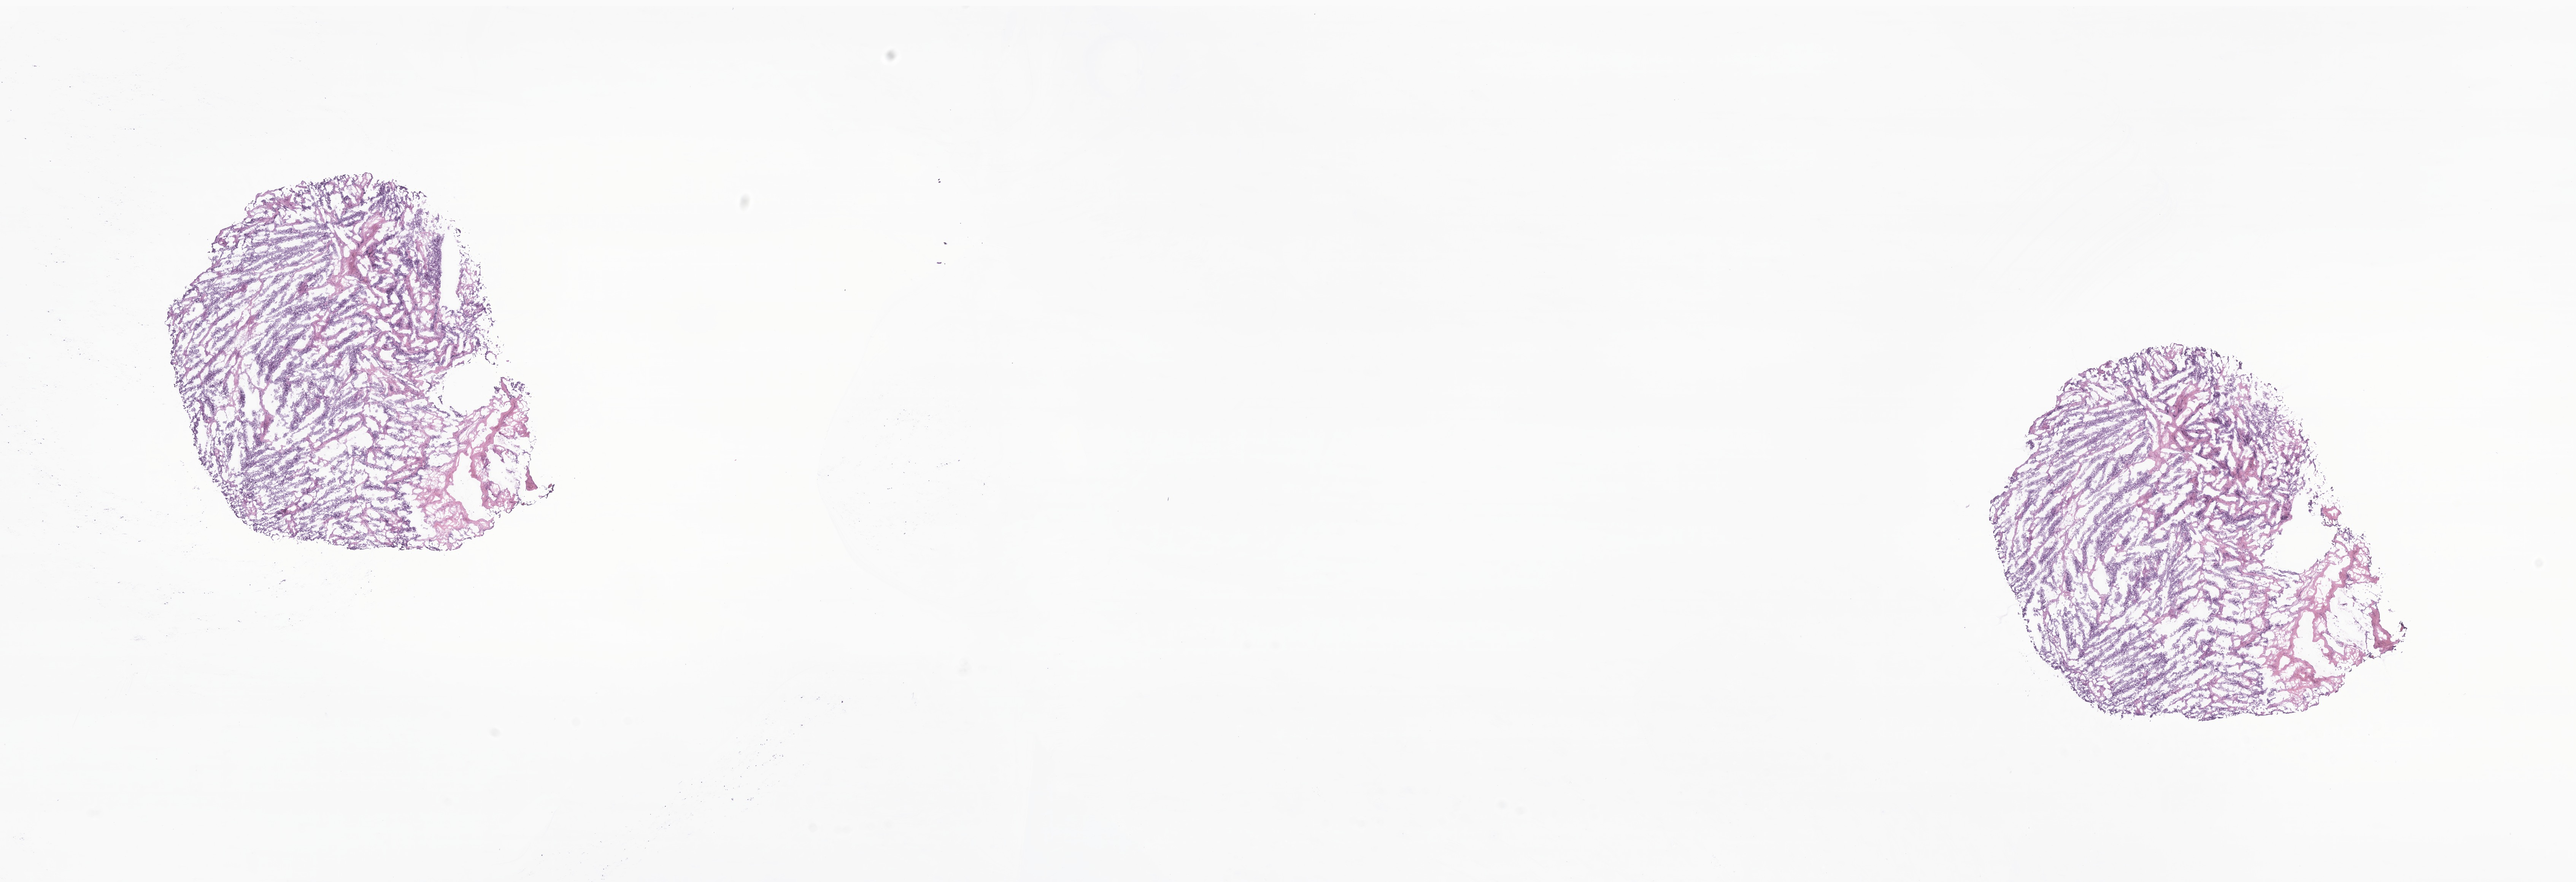
Whole-slide image, H&E stain of tumor tissue from the abdomen, whole scanned area (about 28.6 x 9.8 mm) shown as a low-resolution overview, frozen section (OCT-embedded). Patient: male, age 780 days (about 2.1 years).
Diagnosis (ICD-O-3 morphology term): Neuroblastoma, NOS.